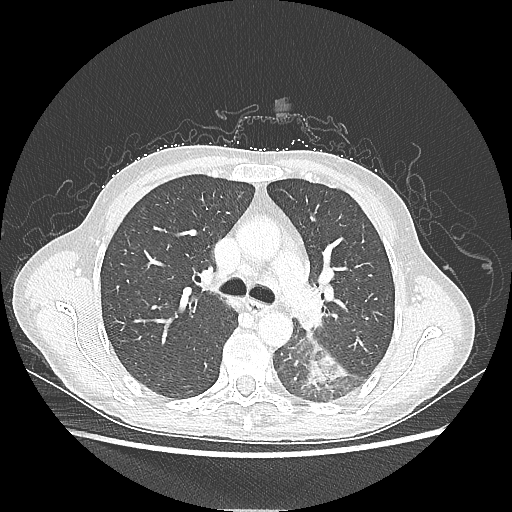
Chest CT, one axial slice; reconstruction kernel LUNG; lung window (W 1500 / L -600 HU); 1.25 mm slice thickness; 512 × 512 image matrix. Patient: female, 53 years. Case-level facts recorded for this patient, not image findings: clinical TNM (as recorded): T3 N0 M0.
Structures marked on this image (rectangle marked by the reading radiologist):
- lung tumour (recorded histology: adenocarcinoma): bounding box <300,346,348,388> (left, top, right, bottom; pixels)